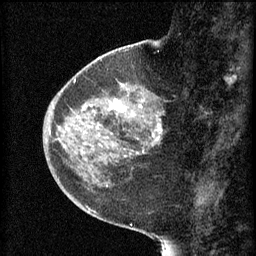
Breast MRI (dynamic contrast-enhanced), one sagittal slice; slice 22 of 60 in the series (ordered by position); 3 images stored at this slice position (order not interpretable as contrast timing); 1.5 T; TE 4.2 ms, TR 8.2 ms; 2 mm slice thickness; 256 × 256 image matrix. Patient: female, 44 years.
Outlined on this slice (semi-automatic segmentation, software-assisted and operator-edited):
- analysis volume of interest (the breast-tissue region the enhancement analysis was run in; not a lesion): bounding box <73,82,166,165> (left, top, right, bottom; pixels)
- tumour enhancement mask (voxels above the 70 % enhancement threshold inside the analysis volume of interest): <74,82,163,155>